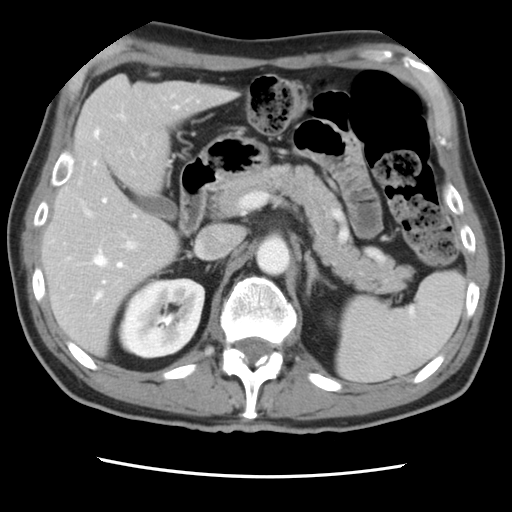
Contrast-enhanced abdominal CT, one axial slice. Slice 47 of 83 in the series (ordered by position). Intravenous contrast given. Soft-tissue window (W 400 / L 40 HU). 5 mm slice thickness. 512 × 512 image matrix, field of view 321 × 321 mm. Male patient, age 69 years. Case-level facts recorded for this patient, not image findings: diagnosis: colorectal cancer liver metastases, imaged before liver resection; multiple liver metastases: yes; largest metastasis: 3.5 cm; disease in both lobes: no.
Outlined on this slice (expert manual segmentation):
- hepatic veins: bounding box [x1, y1, x2, y2] px = [93, 106, 179, 299]
- liver: [44, 77, 233, 353]
- planned liver remnant (the part of the liver to remain after resection): [44, 137, 179, 353]
- portal vein (with intrahepatic branches): [66, 201, 138, 261]